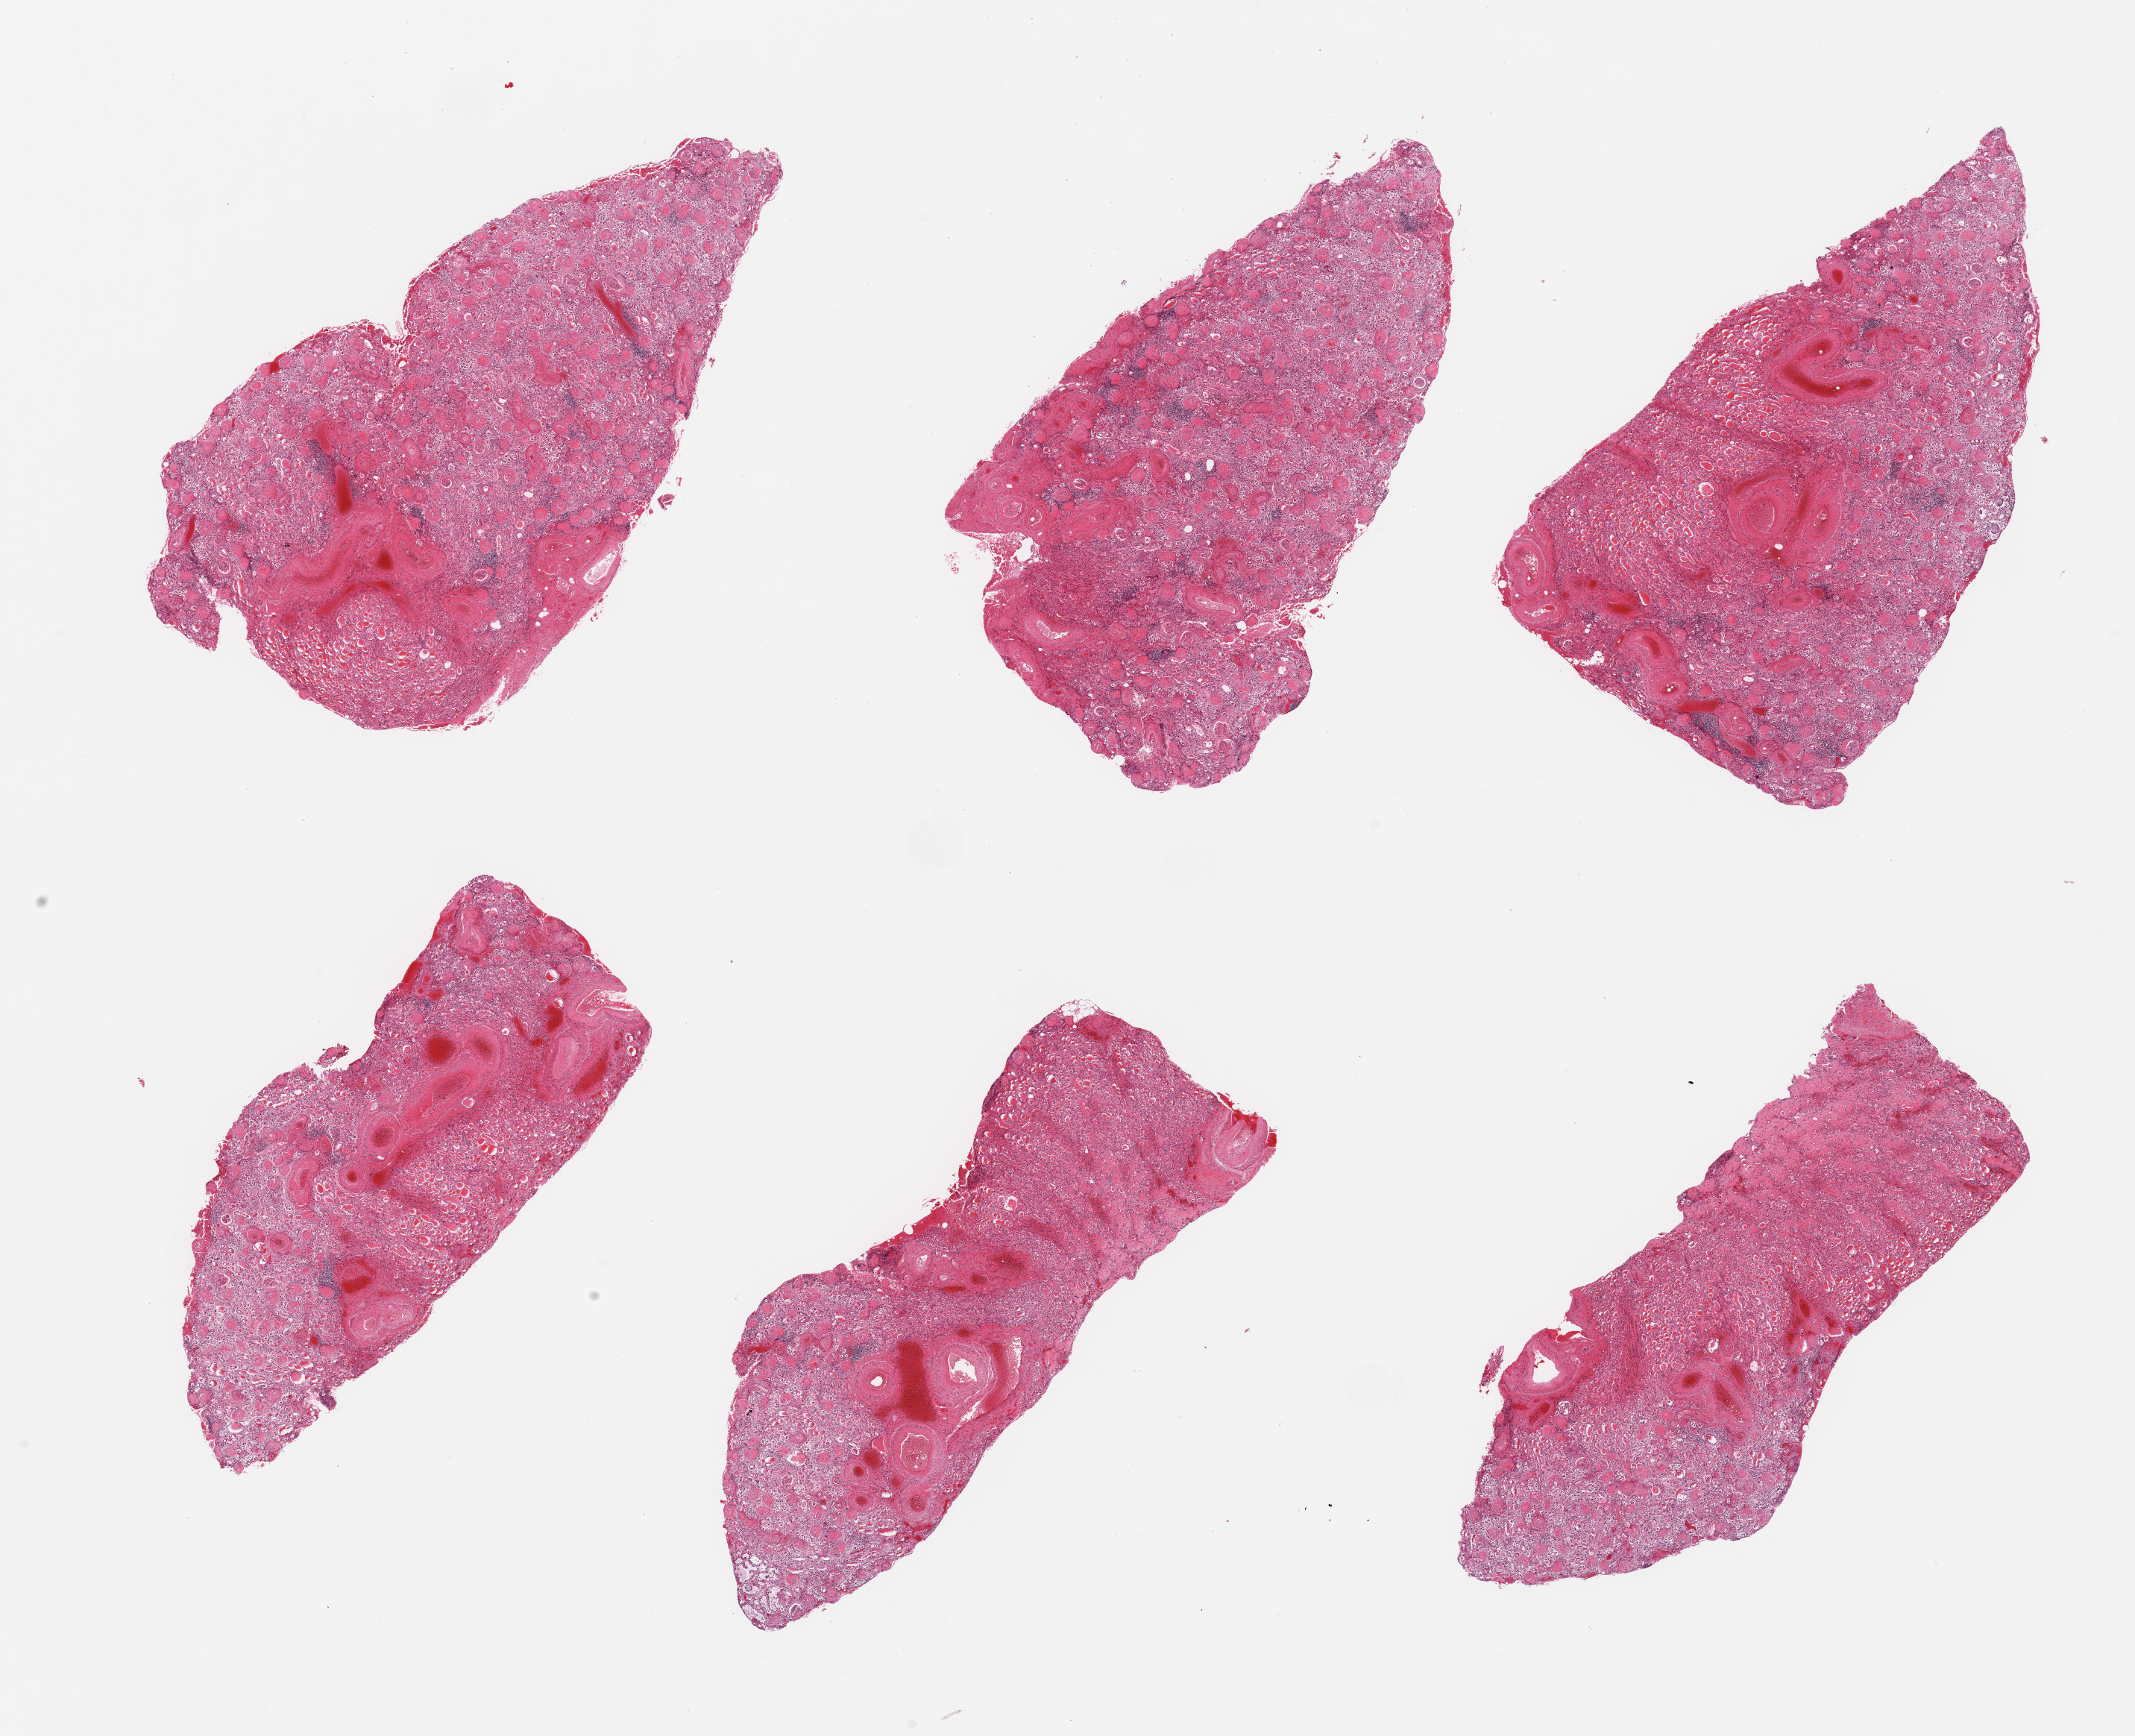
Hematoxylin and eosin (H&E) whole-slide image, shown as a low-resolution overview of the whole scanned area (about 22.6 x 18.4 mm, from a 20x scan). PAXgene-fixed paraffin-embedded (PFPE) section. Section of renal cortex (target tissue). Donor tissue sample. Donor sex: male.
Review note (as recorded): 6 pieces; extensive vascular and glomerular sclerosis; widespread tubular casts (thyroidization).